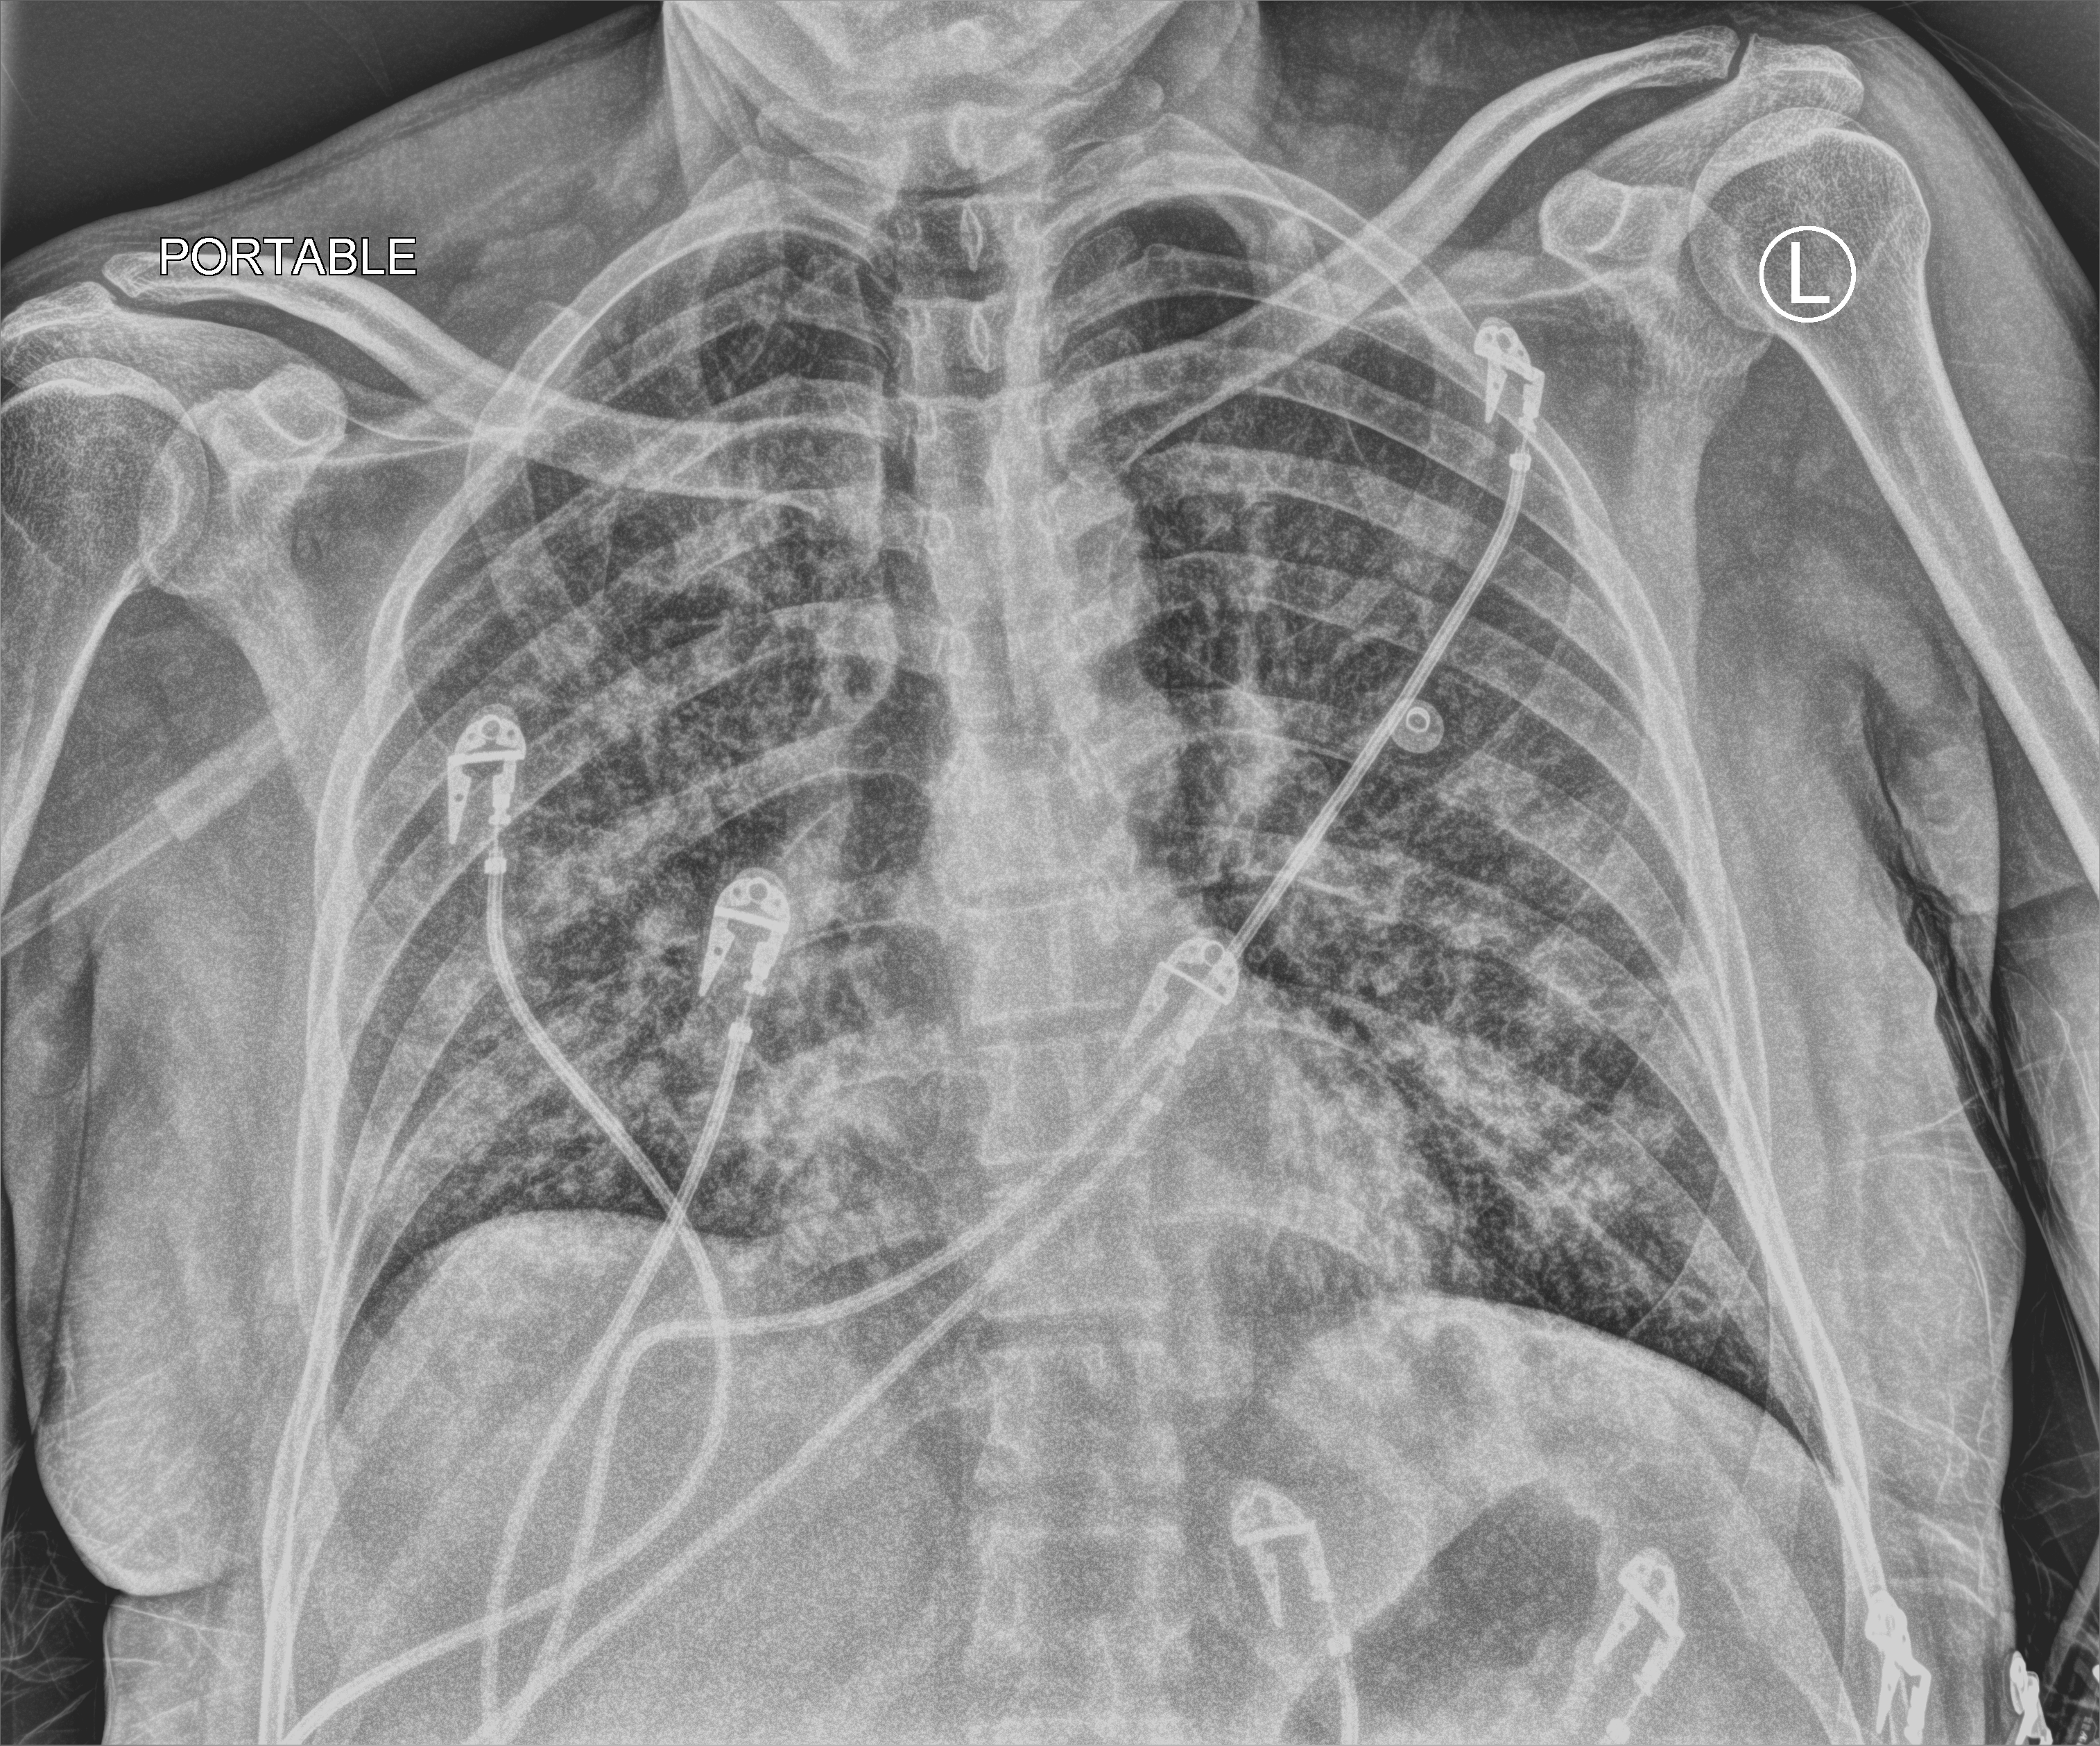
Portable chest radiograph; anteroposterior (AP) projection. Adult patient hospitalised with COVID-19, age 18–59 years.
From the hospital-stay record, not from the radiograph (when in the stay this image was taken is not recorded):
- length of hospital stay: 41 days
- diabetes (admission record): no
- admitted to intensive care during this hospital stay: yes